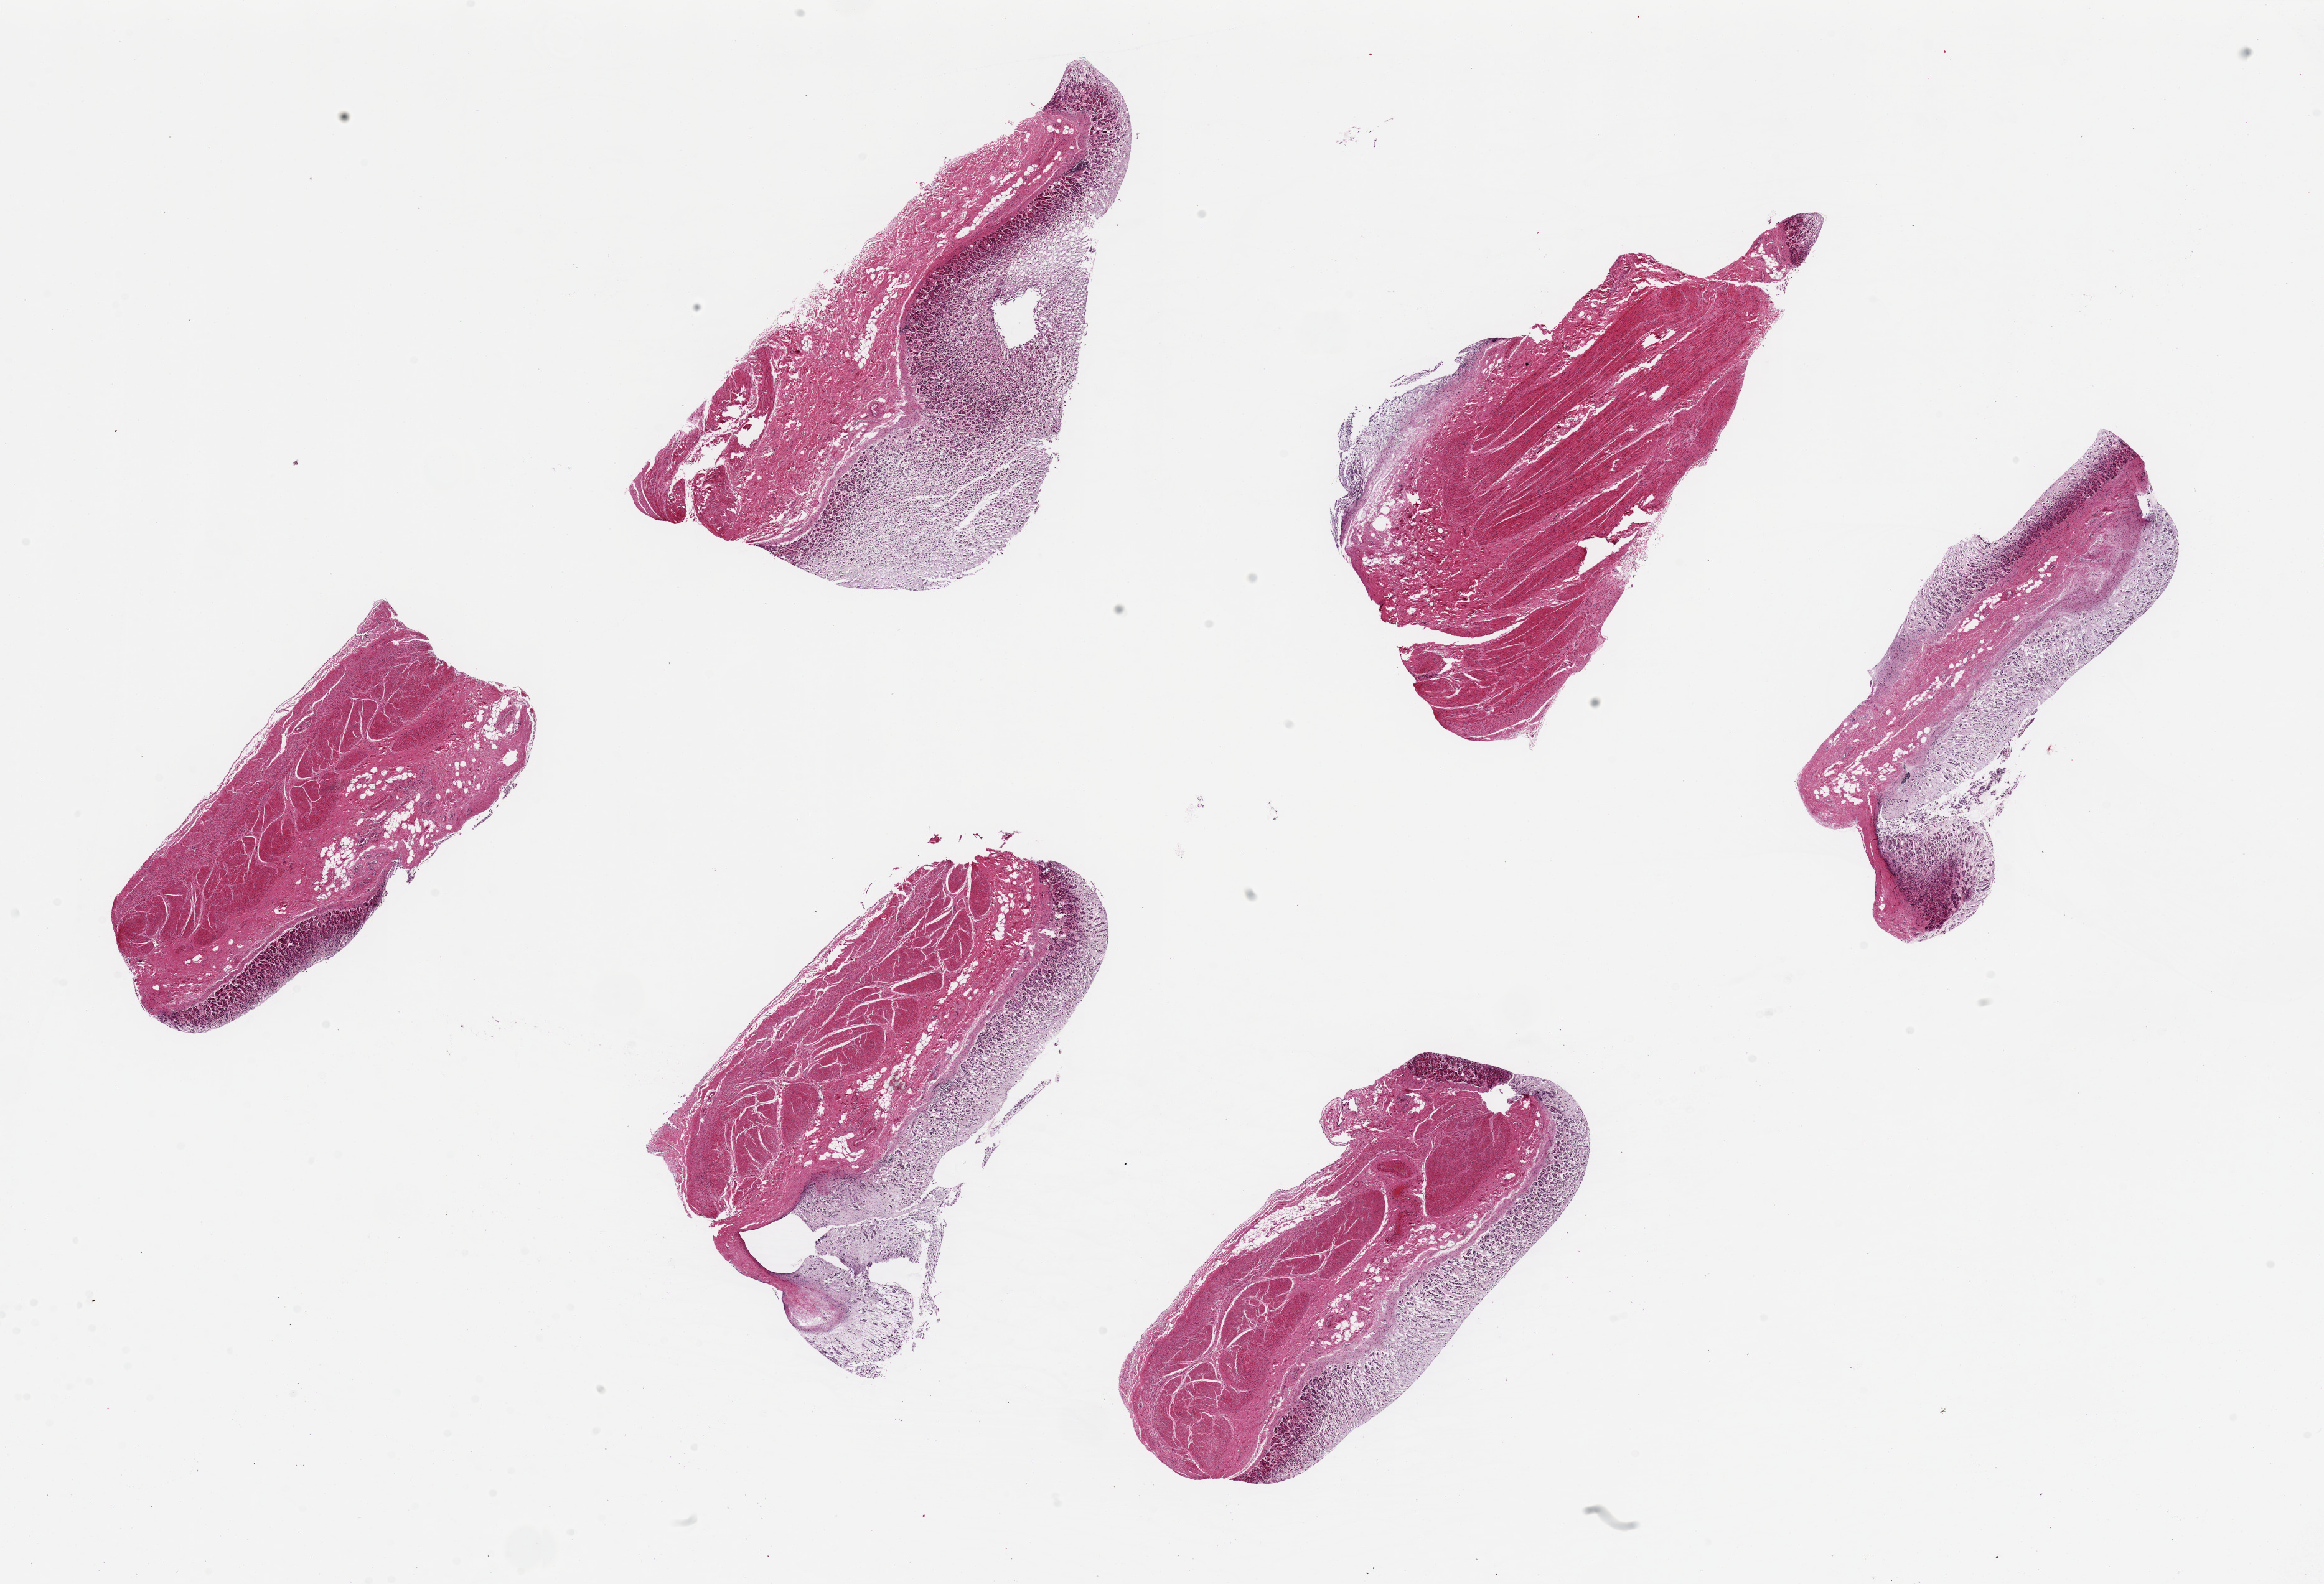
Whole-slide image, hematoxylin and eosin (H&E) stain — shown as a low-resolution overview of the whole scanned area (about 29.5 x 20.1 mm, acquisition: 20x scan), PAXgene-fixed paraffin-embedded (PFPE) section, section of stomach (target tissue), donor tissue sample. Male donor.
Pathologist's review note for this sample: 6 pieces, ~6x2.5mm. Mucosa badly autolyzed, 30-50% of thickness.